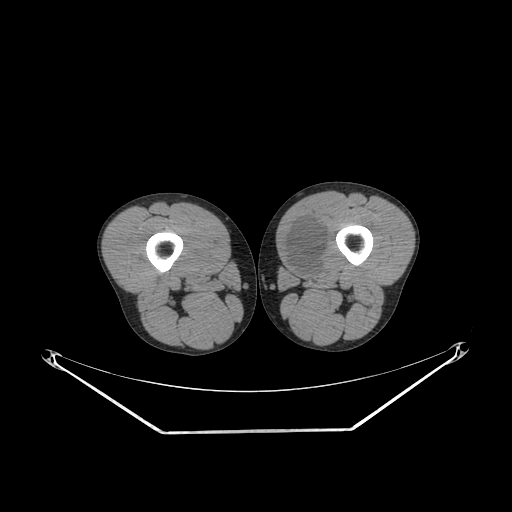
CT of an extremity soft-tissue mass (from a PET/CT study), one axial slice; position 236 of 311 along the scan axis; reconstruction kernel SOFT; 140 kVp; soft-tissue window (W 400 / L 40 HU); 3.75 mm slice thickness; 512 × 512 image matrix, field of view 500 × 500 mm. Male patient. Case-level facts recorded for this patient, not image findings: histological type: mixoid liposarcoma; grade: low; site of the primary tumour: left thigh.
Annotated regions visible in this slice (expert contour drawn on MRI and transferred to this co-registered scan by the dataset authors):
- gross tumour volume (mass): bounding box [x1, y1, x2, y2] px = [283, 216, 328, 277]